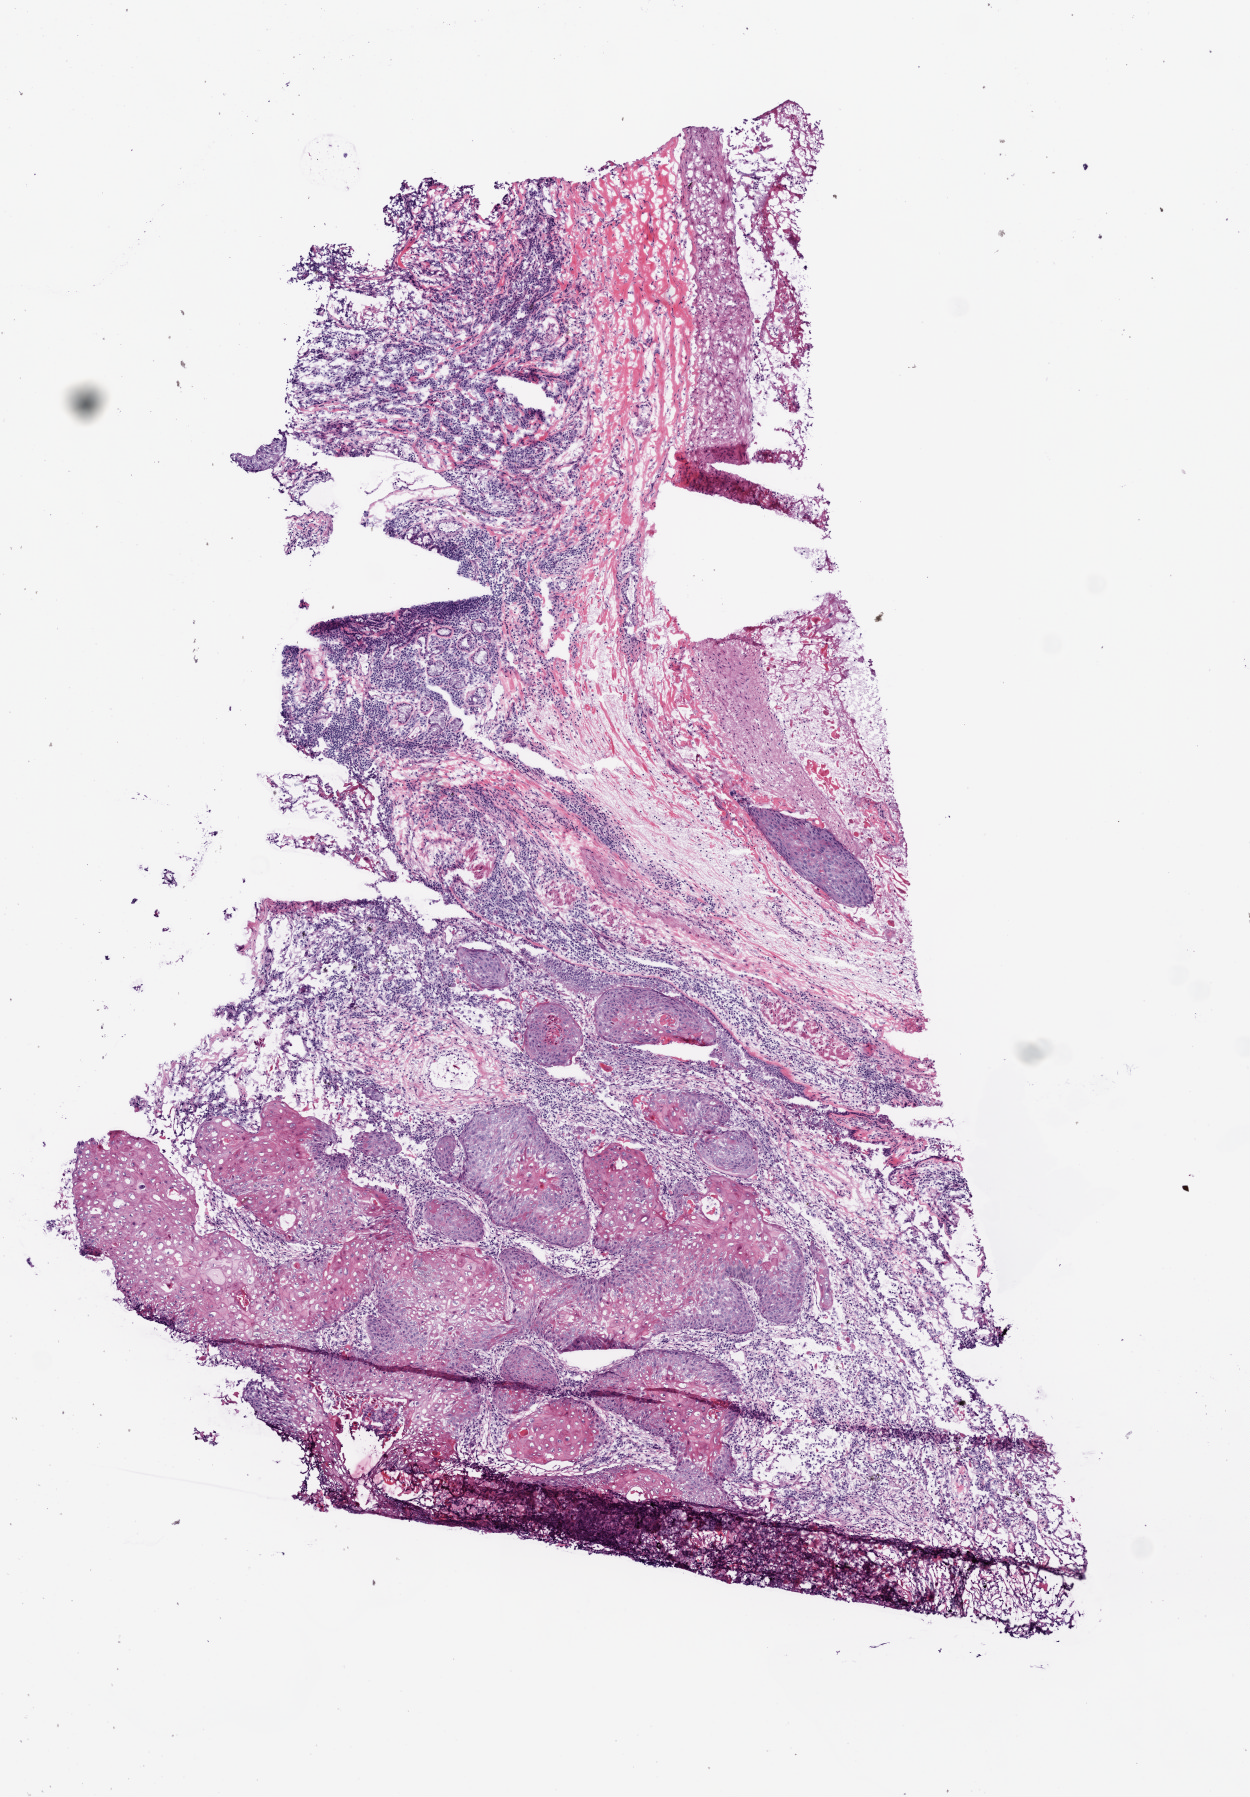
Whole-slide histology image, H&E-stained, whole scanned area (about 5.0 x 7.2 mm, slide scanned at 20x) shown as a low-resolution overview. Frozen section. Primary tumour sample from the lung. Male, age 67 years at initial diagnosis. Slide review estimates, as recorded: tumour cells 60%, tumour nuclei 60%, normal cells 5%, stromal cells 34%, necrosis 1%. Inflammatory infiltration, as recorded: lymphocyte infiltration 20%.
AJCC pathologic stage: IA. Pathologic diagnosis: Squamous cell carcinoma, NOS (upper lobe, lung). Laterality: left.